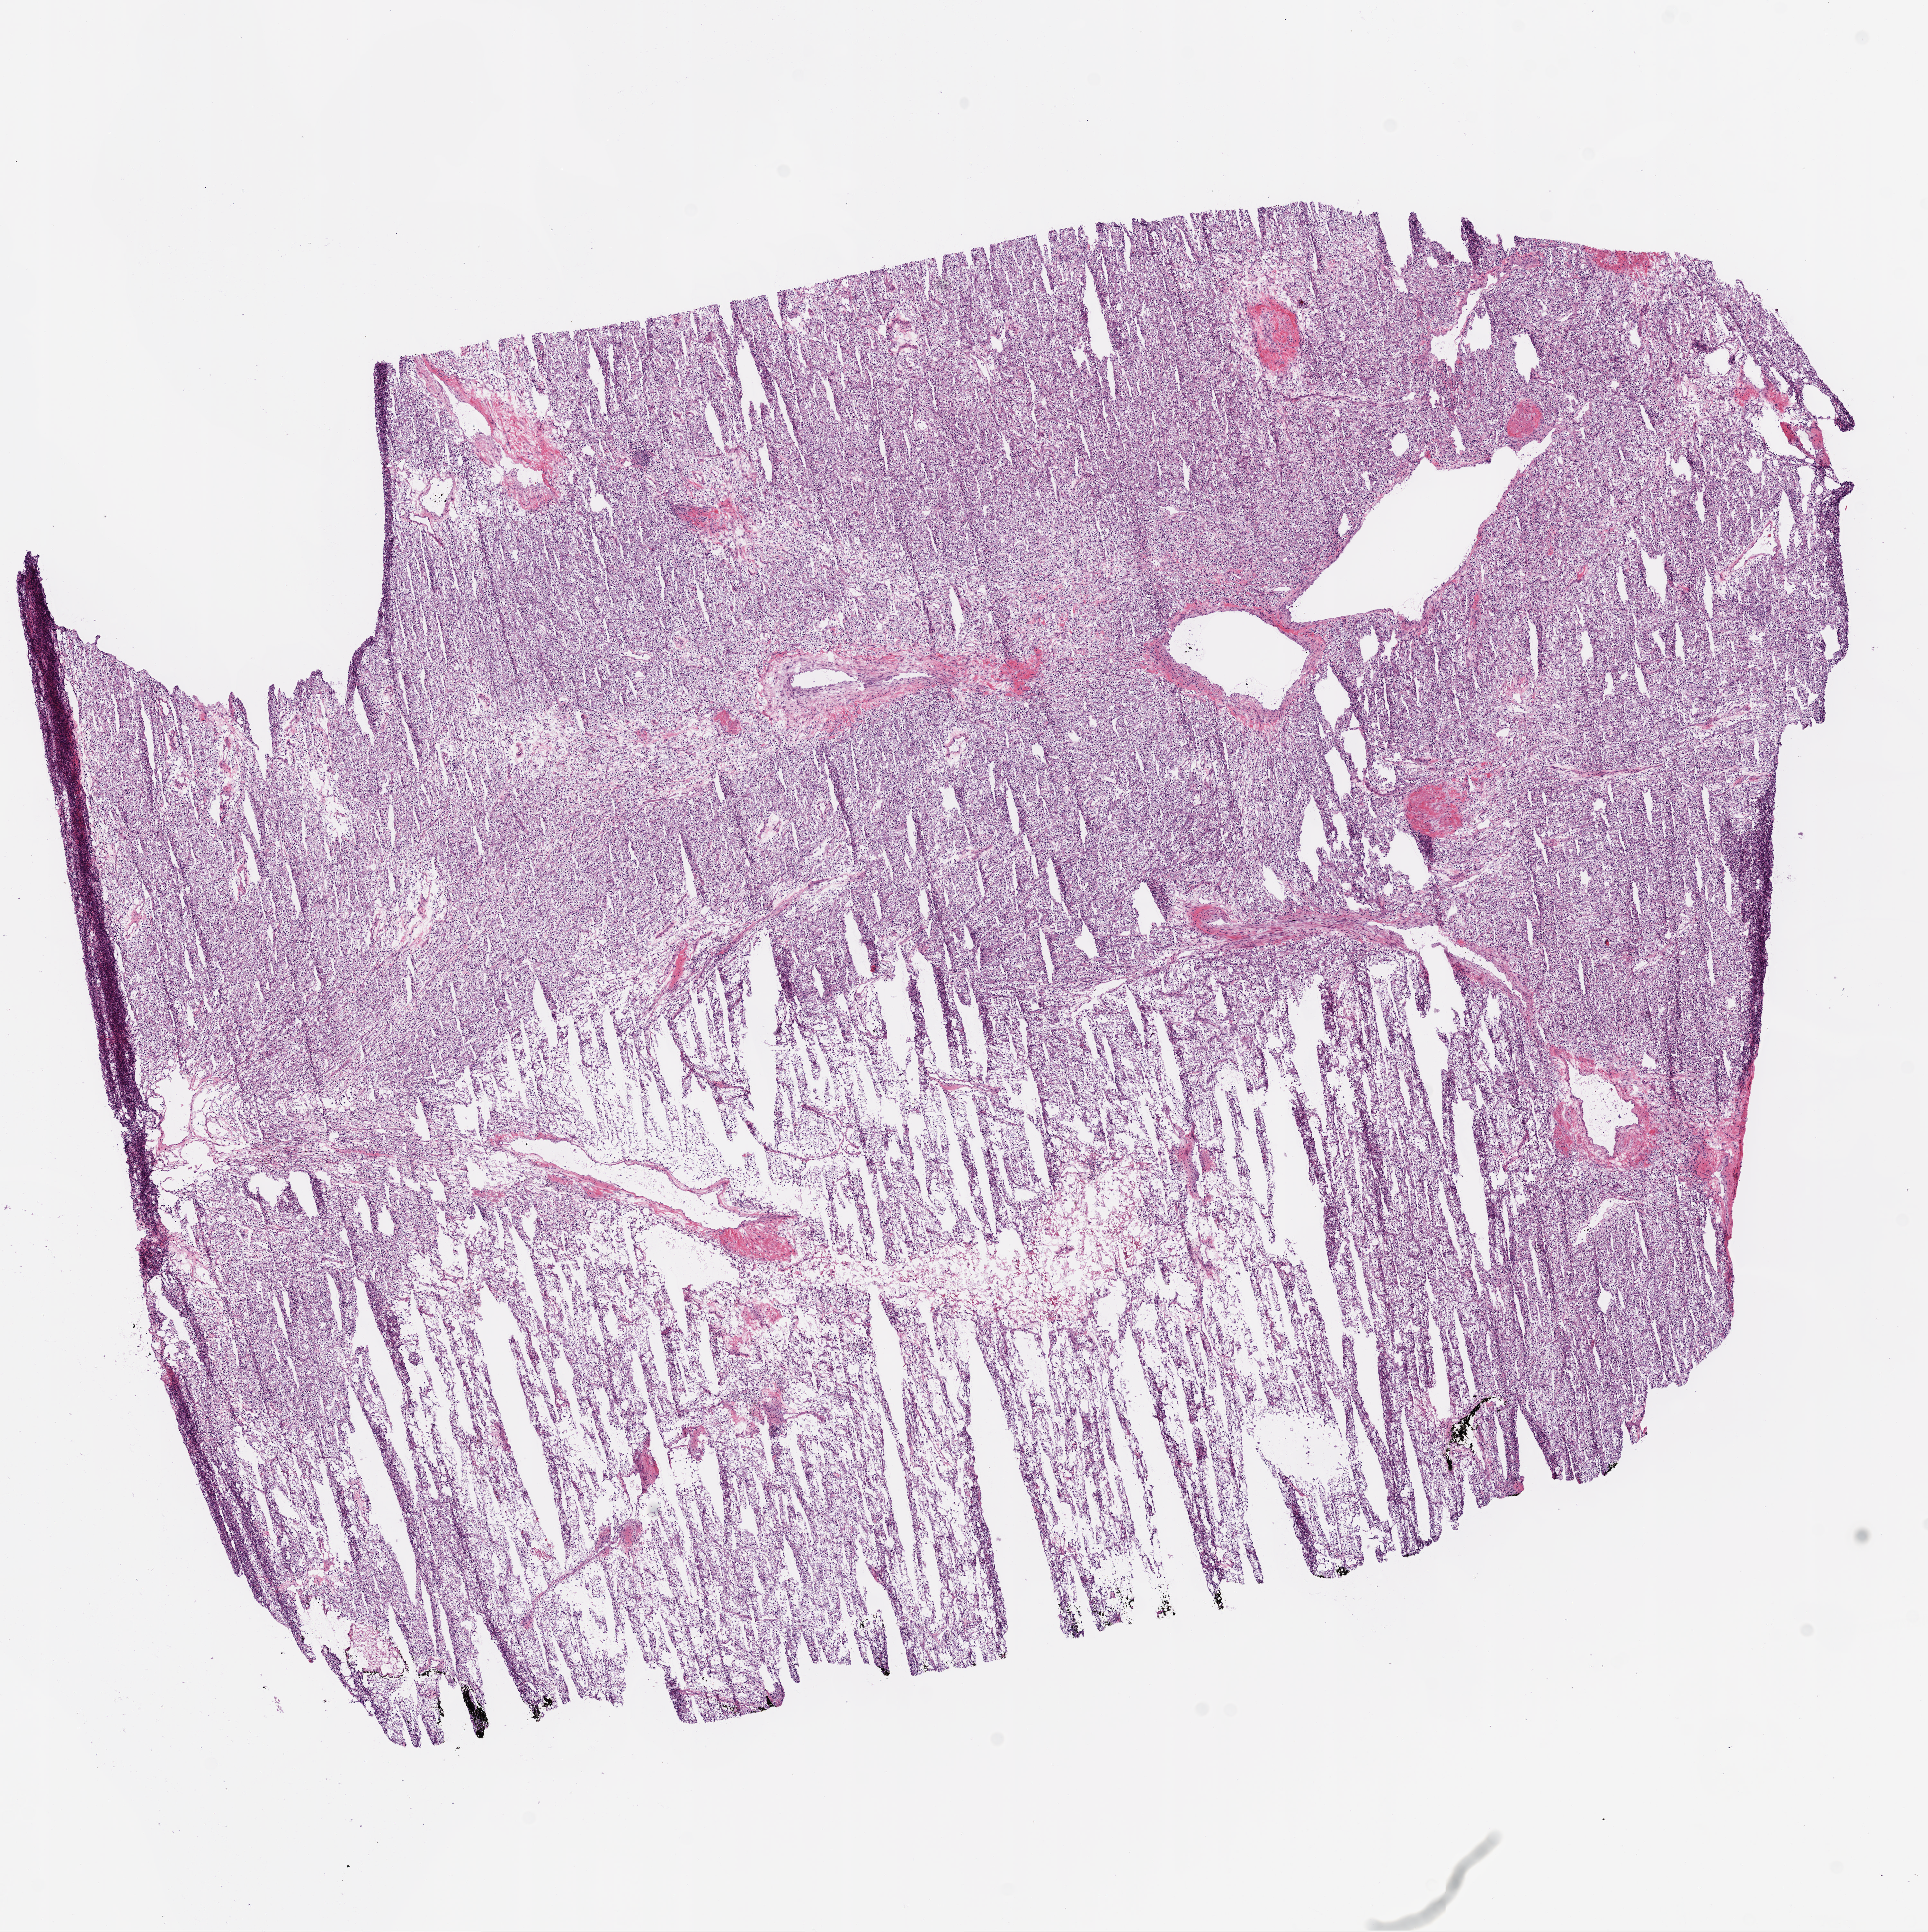
Hematoxylin and eosin (H&E) stained whole-slide image, a low-resolution overview of the entire scanned area, about 12.0 x 12.1 mm (acquisition: 20x scan). Frozen section. Kidney, primary tumour sample. Male, age 53 years at initial diagnosis. Histologic grade: G1 (well differentiated). Pathologist review of this section (percent, as recorded): tumour cells 90%, tumour nuclei 85%, normal cells 0%, stromal cells 5%, necrosis 5%.
AJCC pathologic stage: I. Pathologic diagnosis: Clear cell adenocarcinoma, NOS. Laterality: right. TNM: T1b NX M0.